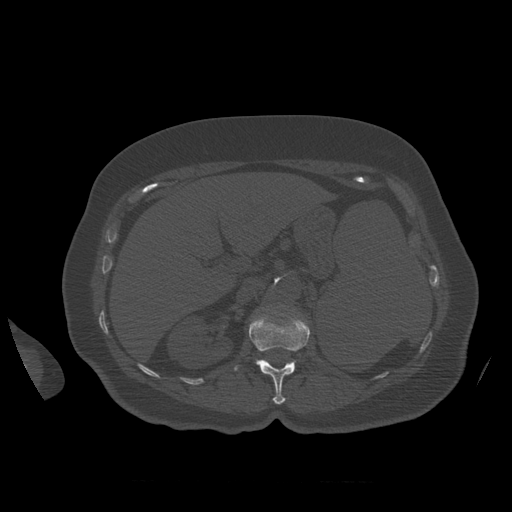
CT including the spine, one axial slice. Position 274 of 399 along the scan axis. Reconstruction kernel STANDARD. 120 kVp. Bone window (W 1800 / L 400 HU). 1.25 mm slice thickness. 512 × 512 image matrix, field of view 404 × 404 mm. Patient age 81 years. From the clinical record (not read from this slice): primary cancer: renal; vertebrae with lytic lesions (as recorded): L1.
Structures marked on this image (semi-automatically segmented with operator editing):
- L1 vertebra: bounding box <234,311,310,405> (left, top, right, bottom; pixels)